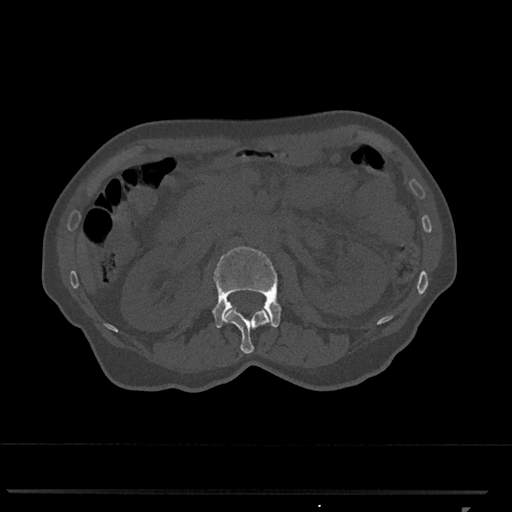
CT including the spine, one axial slice. Slice 366 of 793 in the series (ordered by position). Bone window (W 1800 / L 400 HU). 0.5 mm slice thickness. 512 × 512 image matrix. Female patient, age 62 years. Case-level facts recorded for this patient, not image findings: primary cancer: renal.
Annotated regions visible in this slice (semi-automatically segmented with operator editing):
- L1 vertebra: box from (x=223, y=307) to (x=271, y=354) px
- L2 vertebra: (x=213, y=246)–(x=281, y=328)